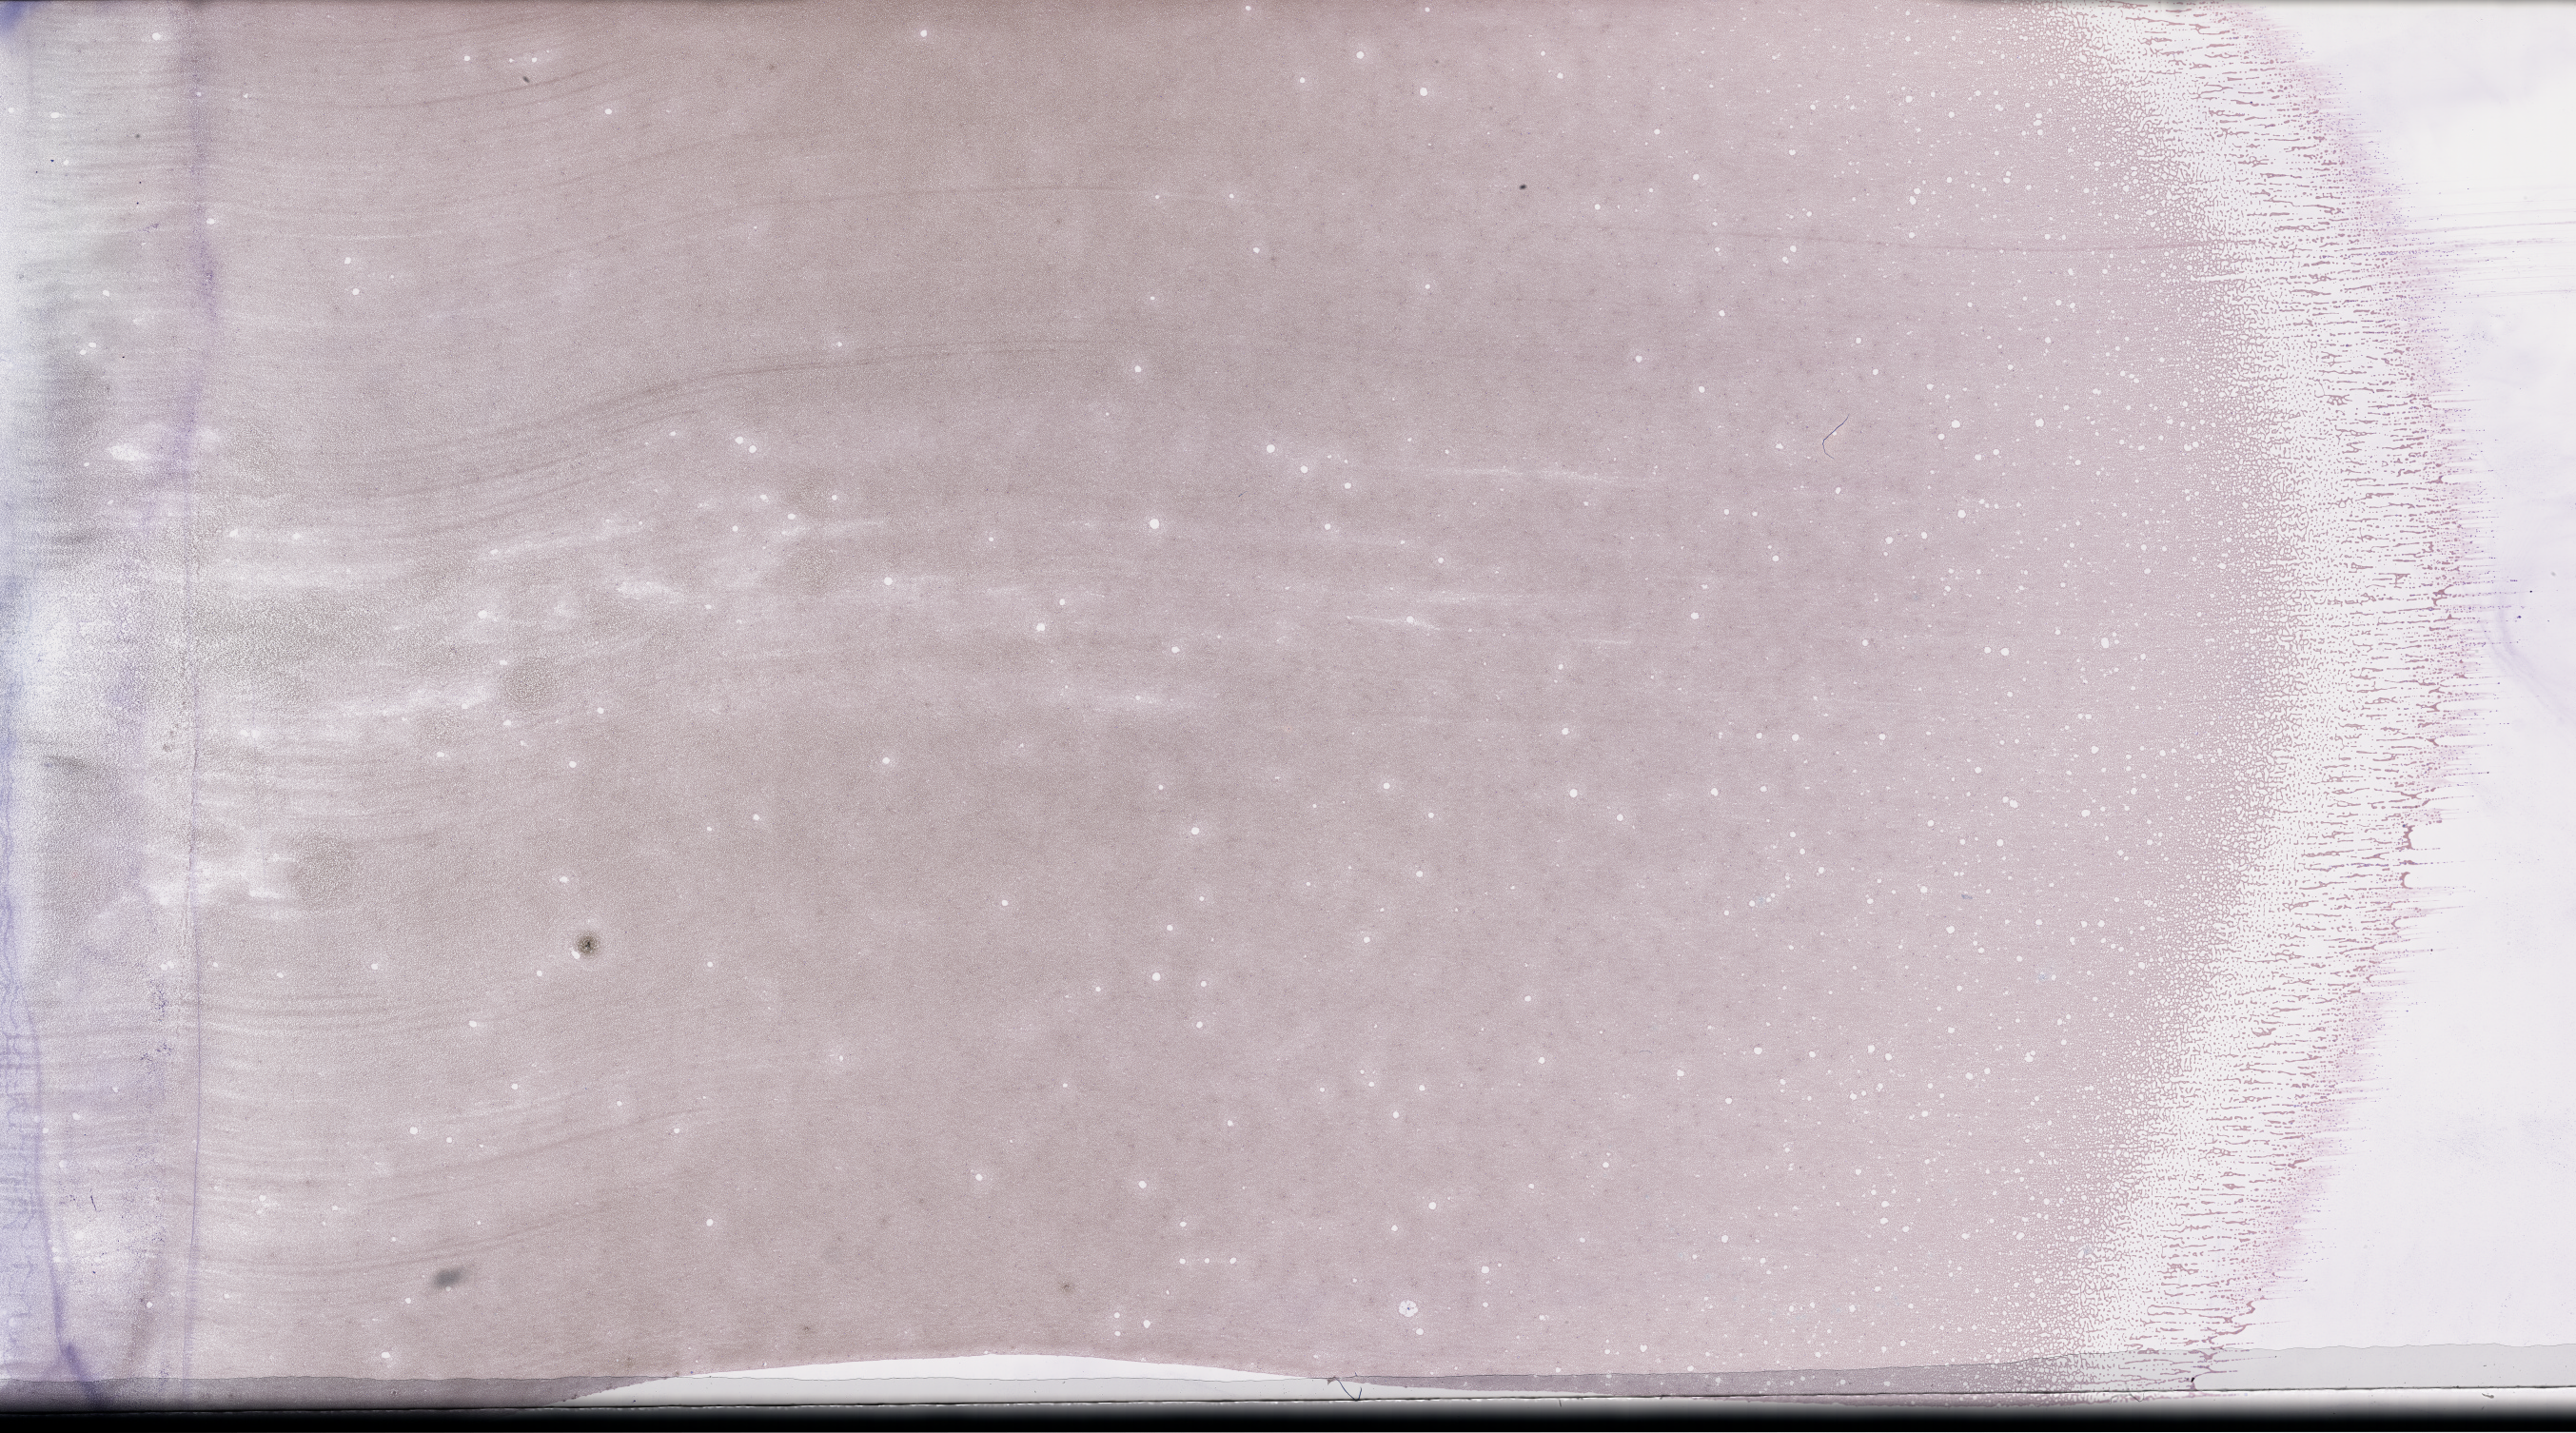
Whole-slide image of a whole blood smear, Wright–Giemsa stain, whole scanned area (about 43.7 x 24.3 mm) shown as a low-resolution overview. Smear from an EDTA sample. Specimen time point: collected on treatment. Patient: female.
From a patient with: Plasma Cell Myeloma.